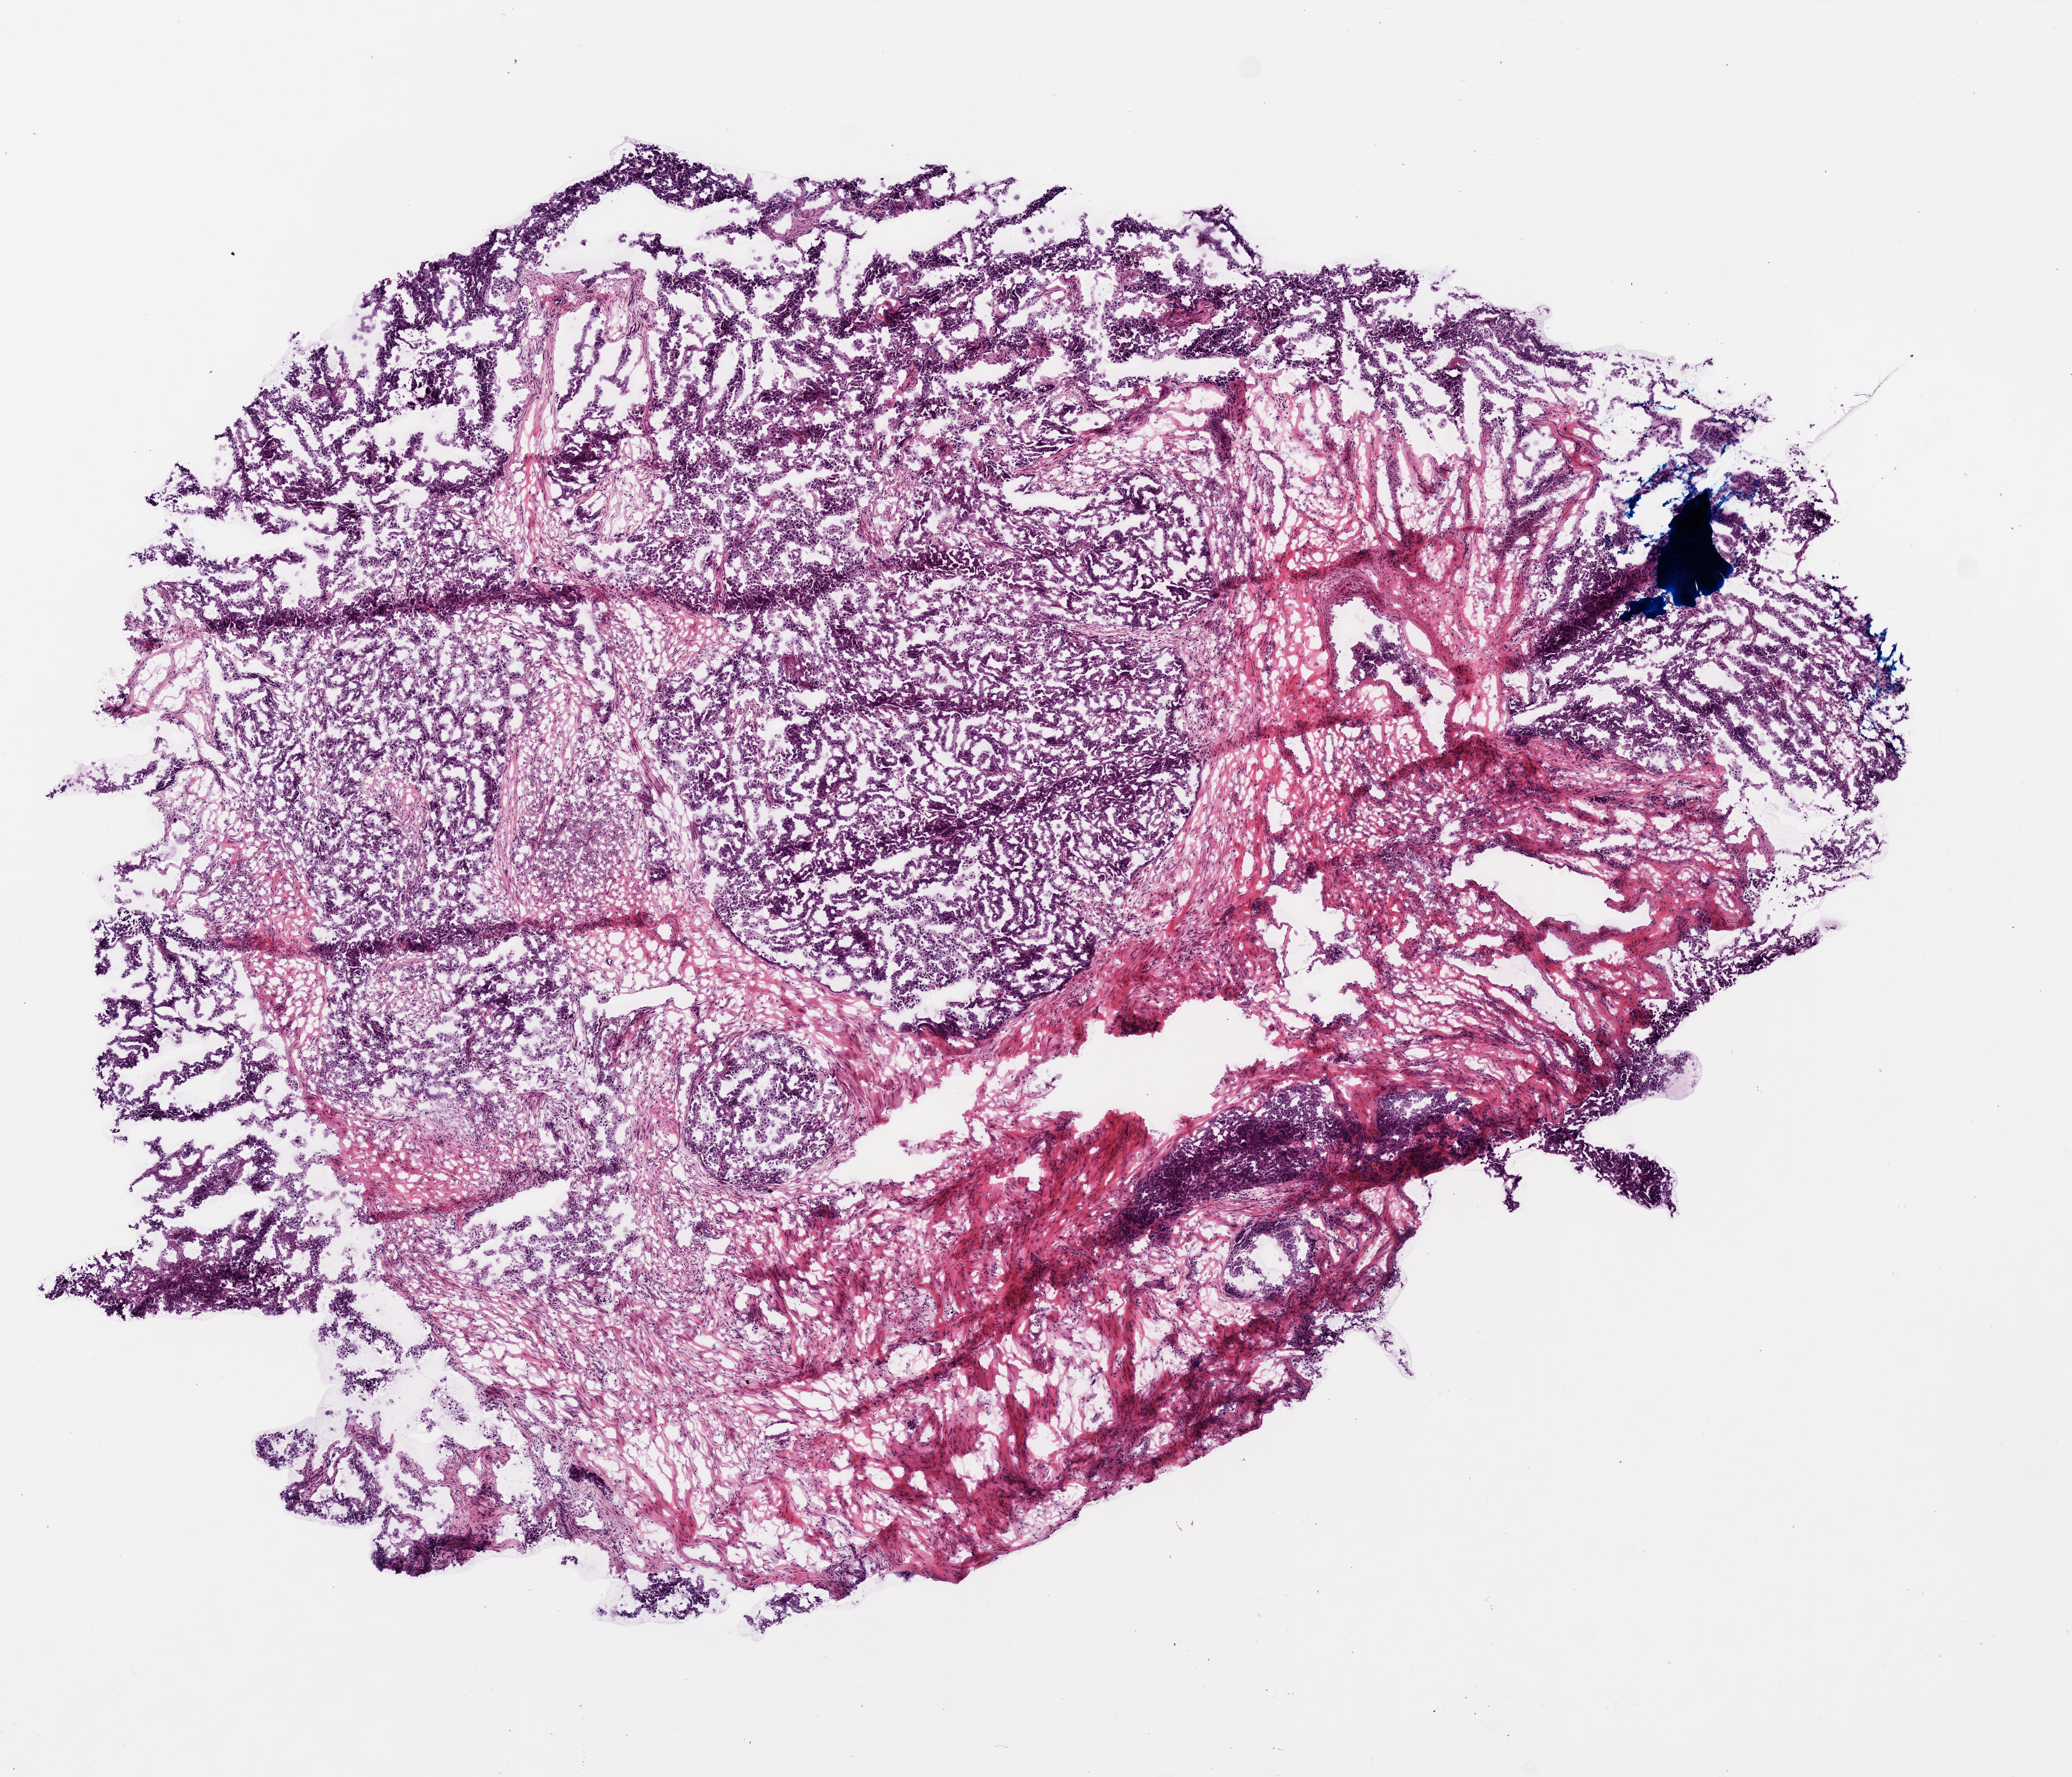
Whole-slide histology image, H&E-stained — whole scanned area (about 8.0 x 6.9 mm, slide scanned at 20x) shown as a low-resolution overview. Frozen section from the top of the tissue portion. Ovary, primary tumour sample. Female patient; age at initial diagnosis 45 years. Slide review estimates, as recorded: tumour nuclei 95%, necrosis 0%.
Diagnosis: Serous cystadenocarcinoma, NOS.